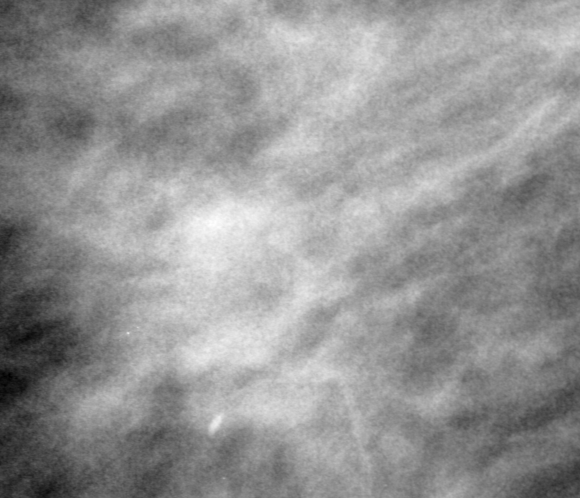
Crop from a digitized film mammogram around one marked abnormality; right breast; MLO view; BI-RADS breast density category 2 (scale 1–4).
Marked abnormality: mass, shape irregular, margins obscured; BI-RADS assessment category 3; subtlety rating 3 on a 1 (subtle) to 5 (obvious) scale; pathology (as recorded): malignant.